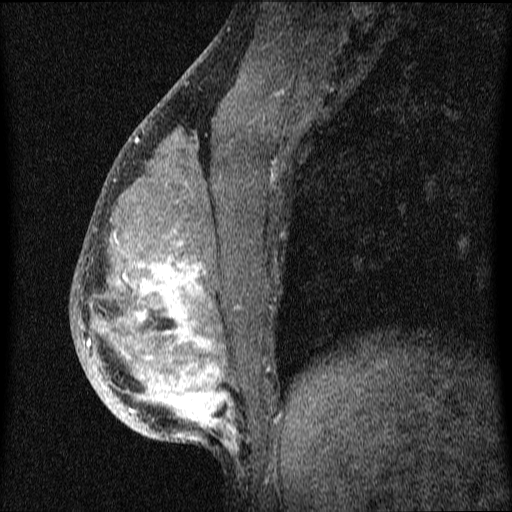
Breast MRI (dynamic contrast-enhanced), one sagittal slice; slice 28 of 64 in the series (ordered by position); dynamic contrast-enhanced series, image 2 of 4 at this slice position (ordered by acquisition); 1.5 T; TE 4.2 ms, TR 9.1 ms; 2 mm slice thickness; 512 × 512 image matrix. Patient: female, 33 years.
Outlined on this slice (semi-automatic segmentation, software-assisted and operator-edited):
- analysis volume of interest (the breast-tissue region the enhancement analysis was run in; not a lesion): bounding box (x1, y1, x2, y2) in pixels: (71, 151, 336, 457)
- tumour enhancement mask (voxels above the 70 % enhancement threshold inside the analysis volume of interest): (87, 196, 234, 445)